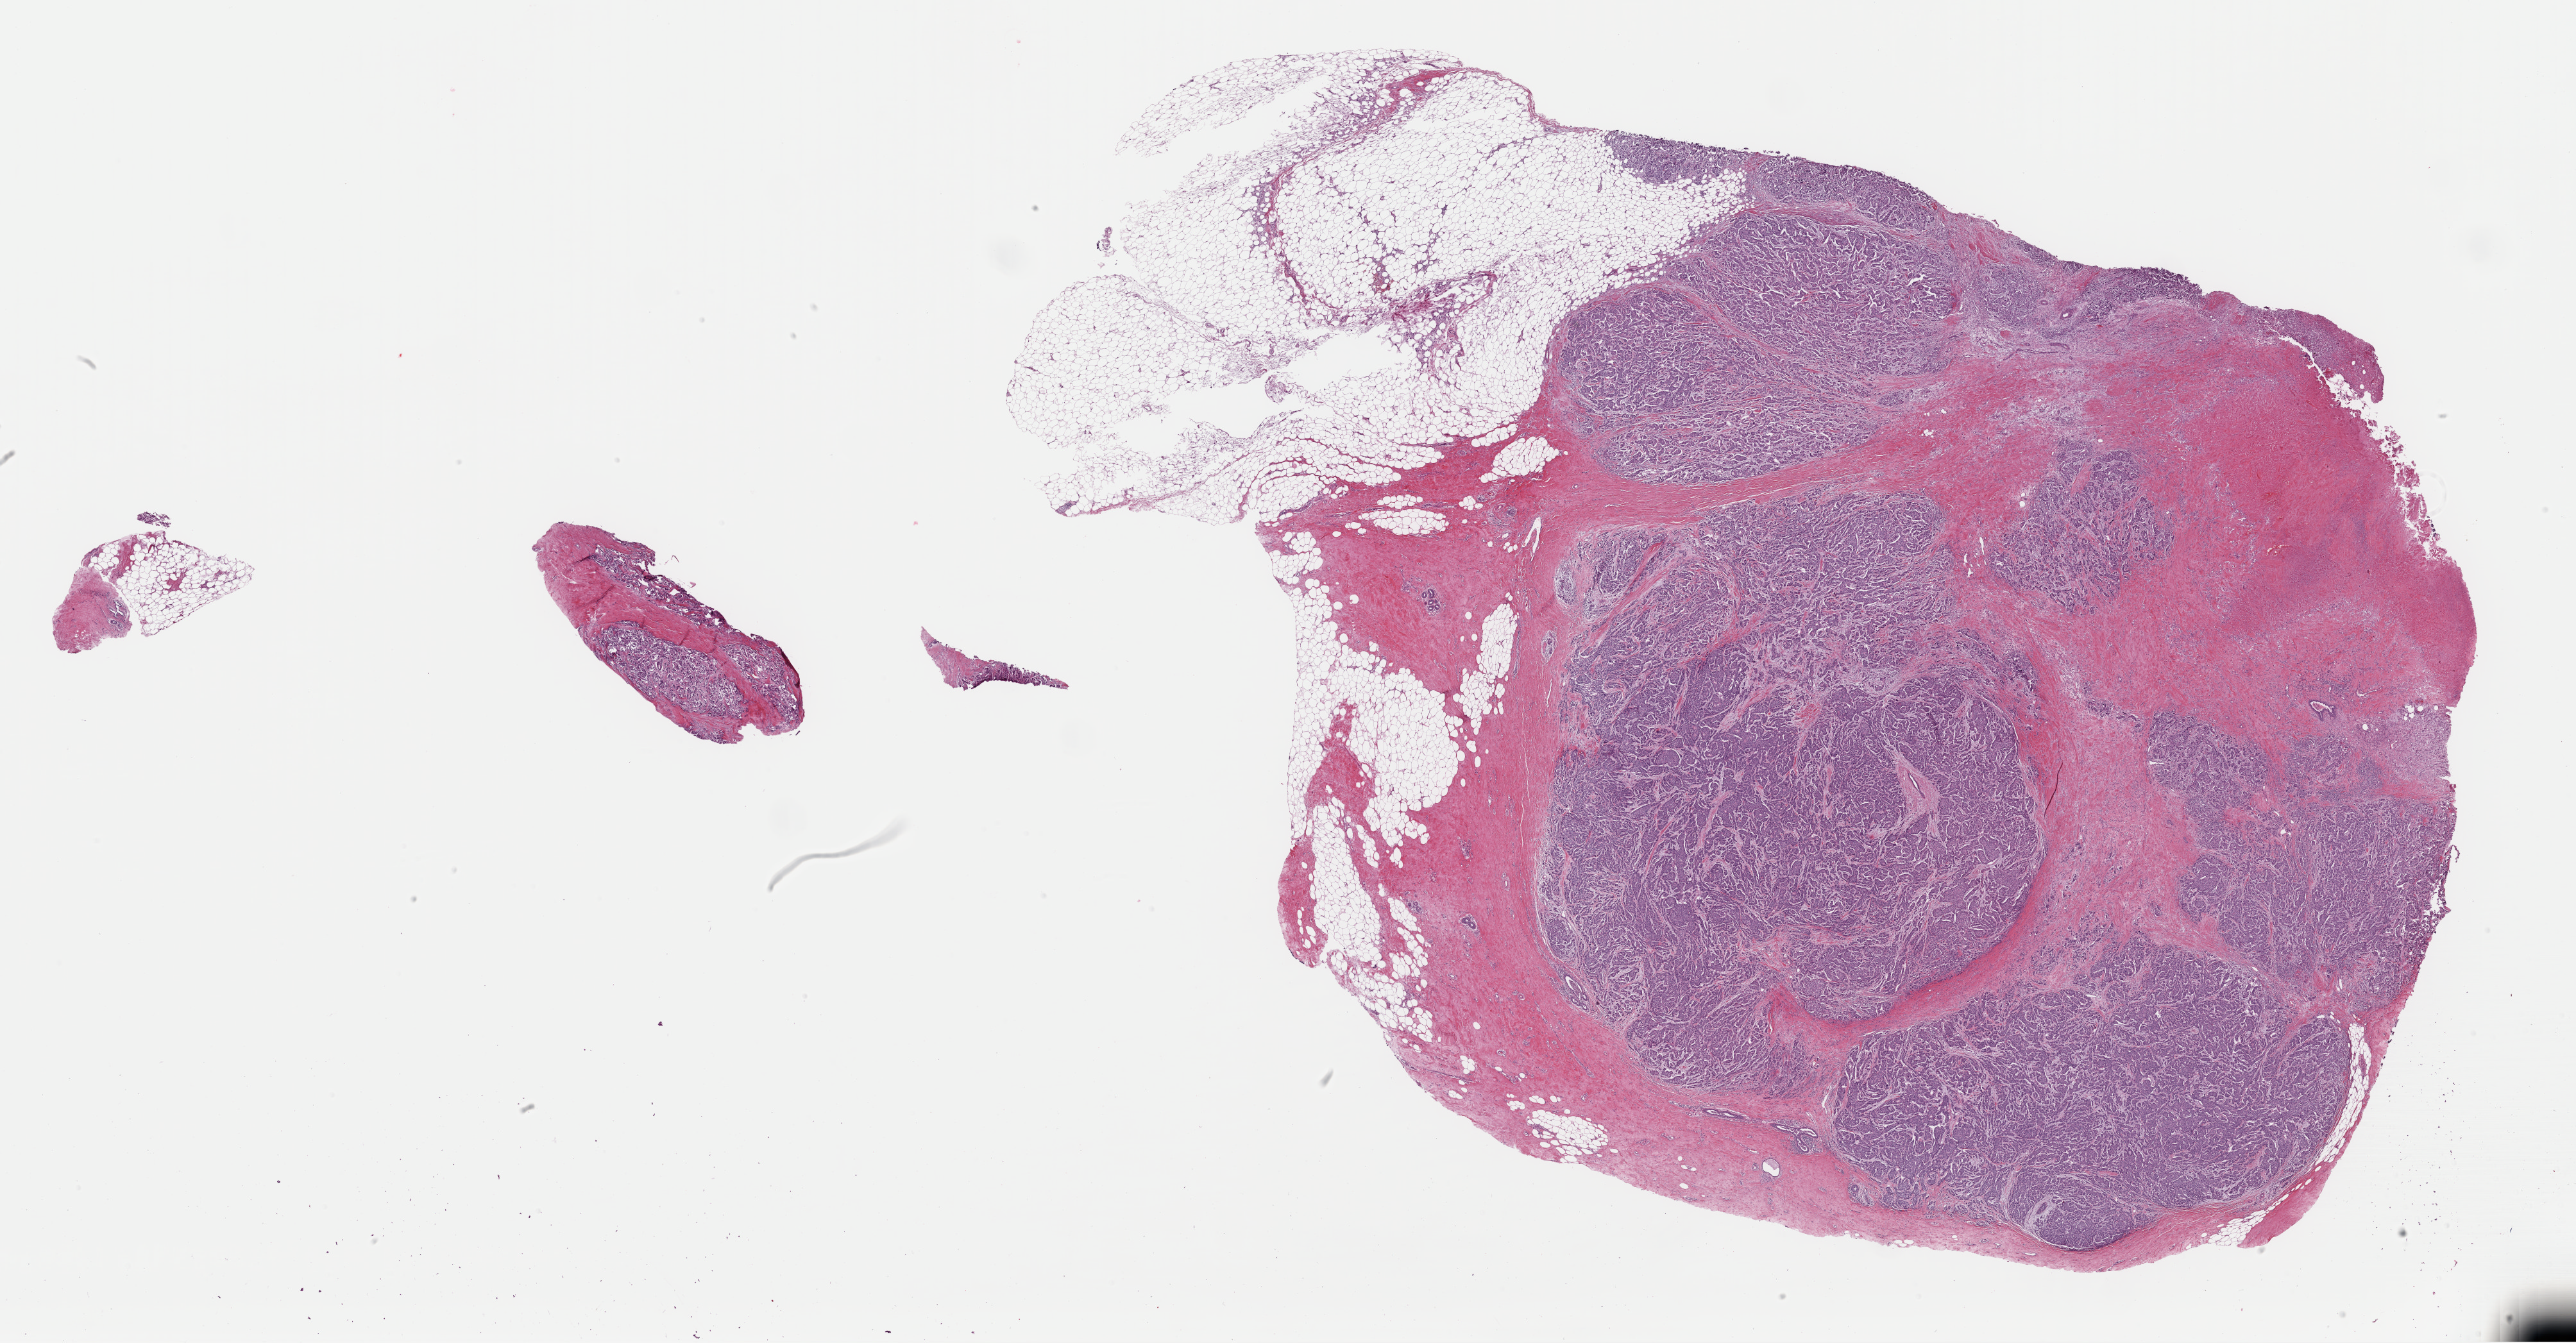
Whole-slide histology image, H&E-stained, a low-resolution overview of the entire scanned area, about 31.7 x 16.5 mm (acquisition: 40x scan); formalin-fixed paraffin-embedded (FFPE) diagnostic section; primary tumour sample from the breast. Patient: female, age at initial diagnosis 47 years.
Laterality: left. AJCC pathologic stage: IIIA. Pathologic diagnosis: Infiltrating duct carcinoma, NOS. Lymph nodes positive (case pathology): 4 of 16 examined.